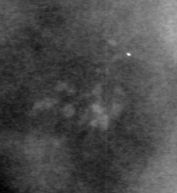
Crop from a digitized film mammogram around one marked abnormality; left breast; MLO view; BI-RADS breast density category 3 (scale 1–4).
- Marked abnormality: calcifications, morphology pleomorphic, distribution clustered; BI-RADS assessment category 4; pathology (as recorded): benign.